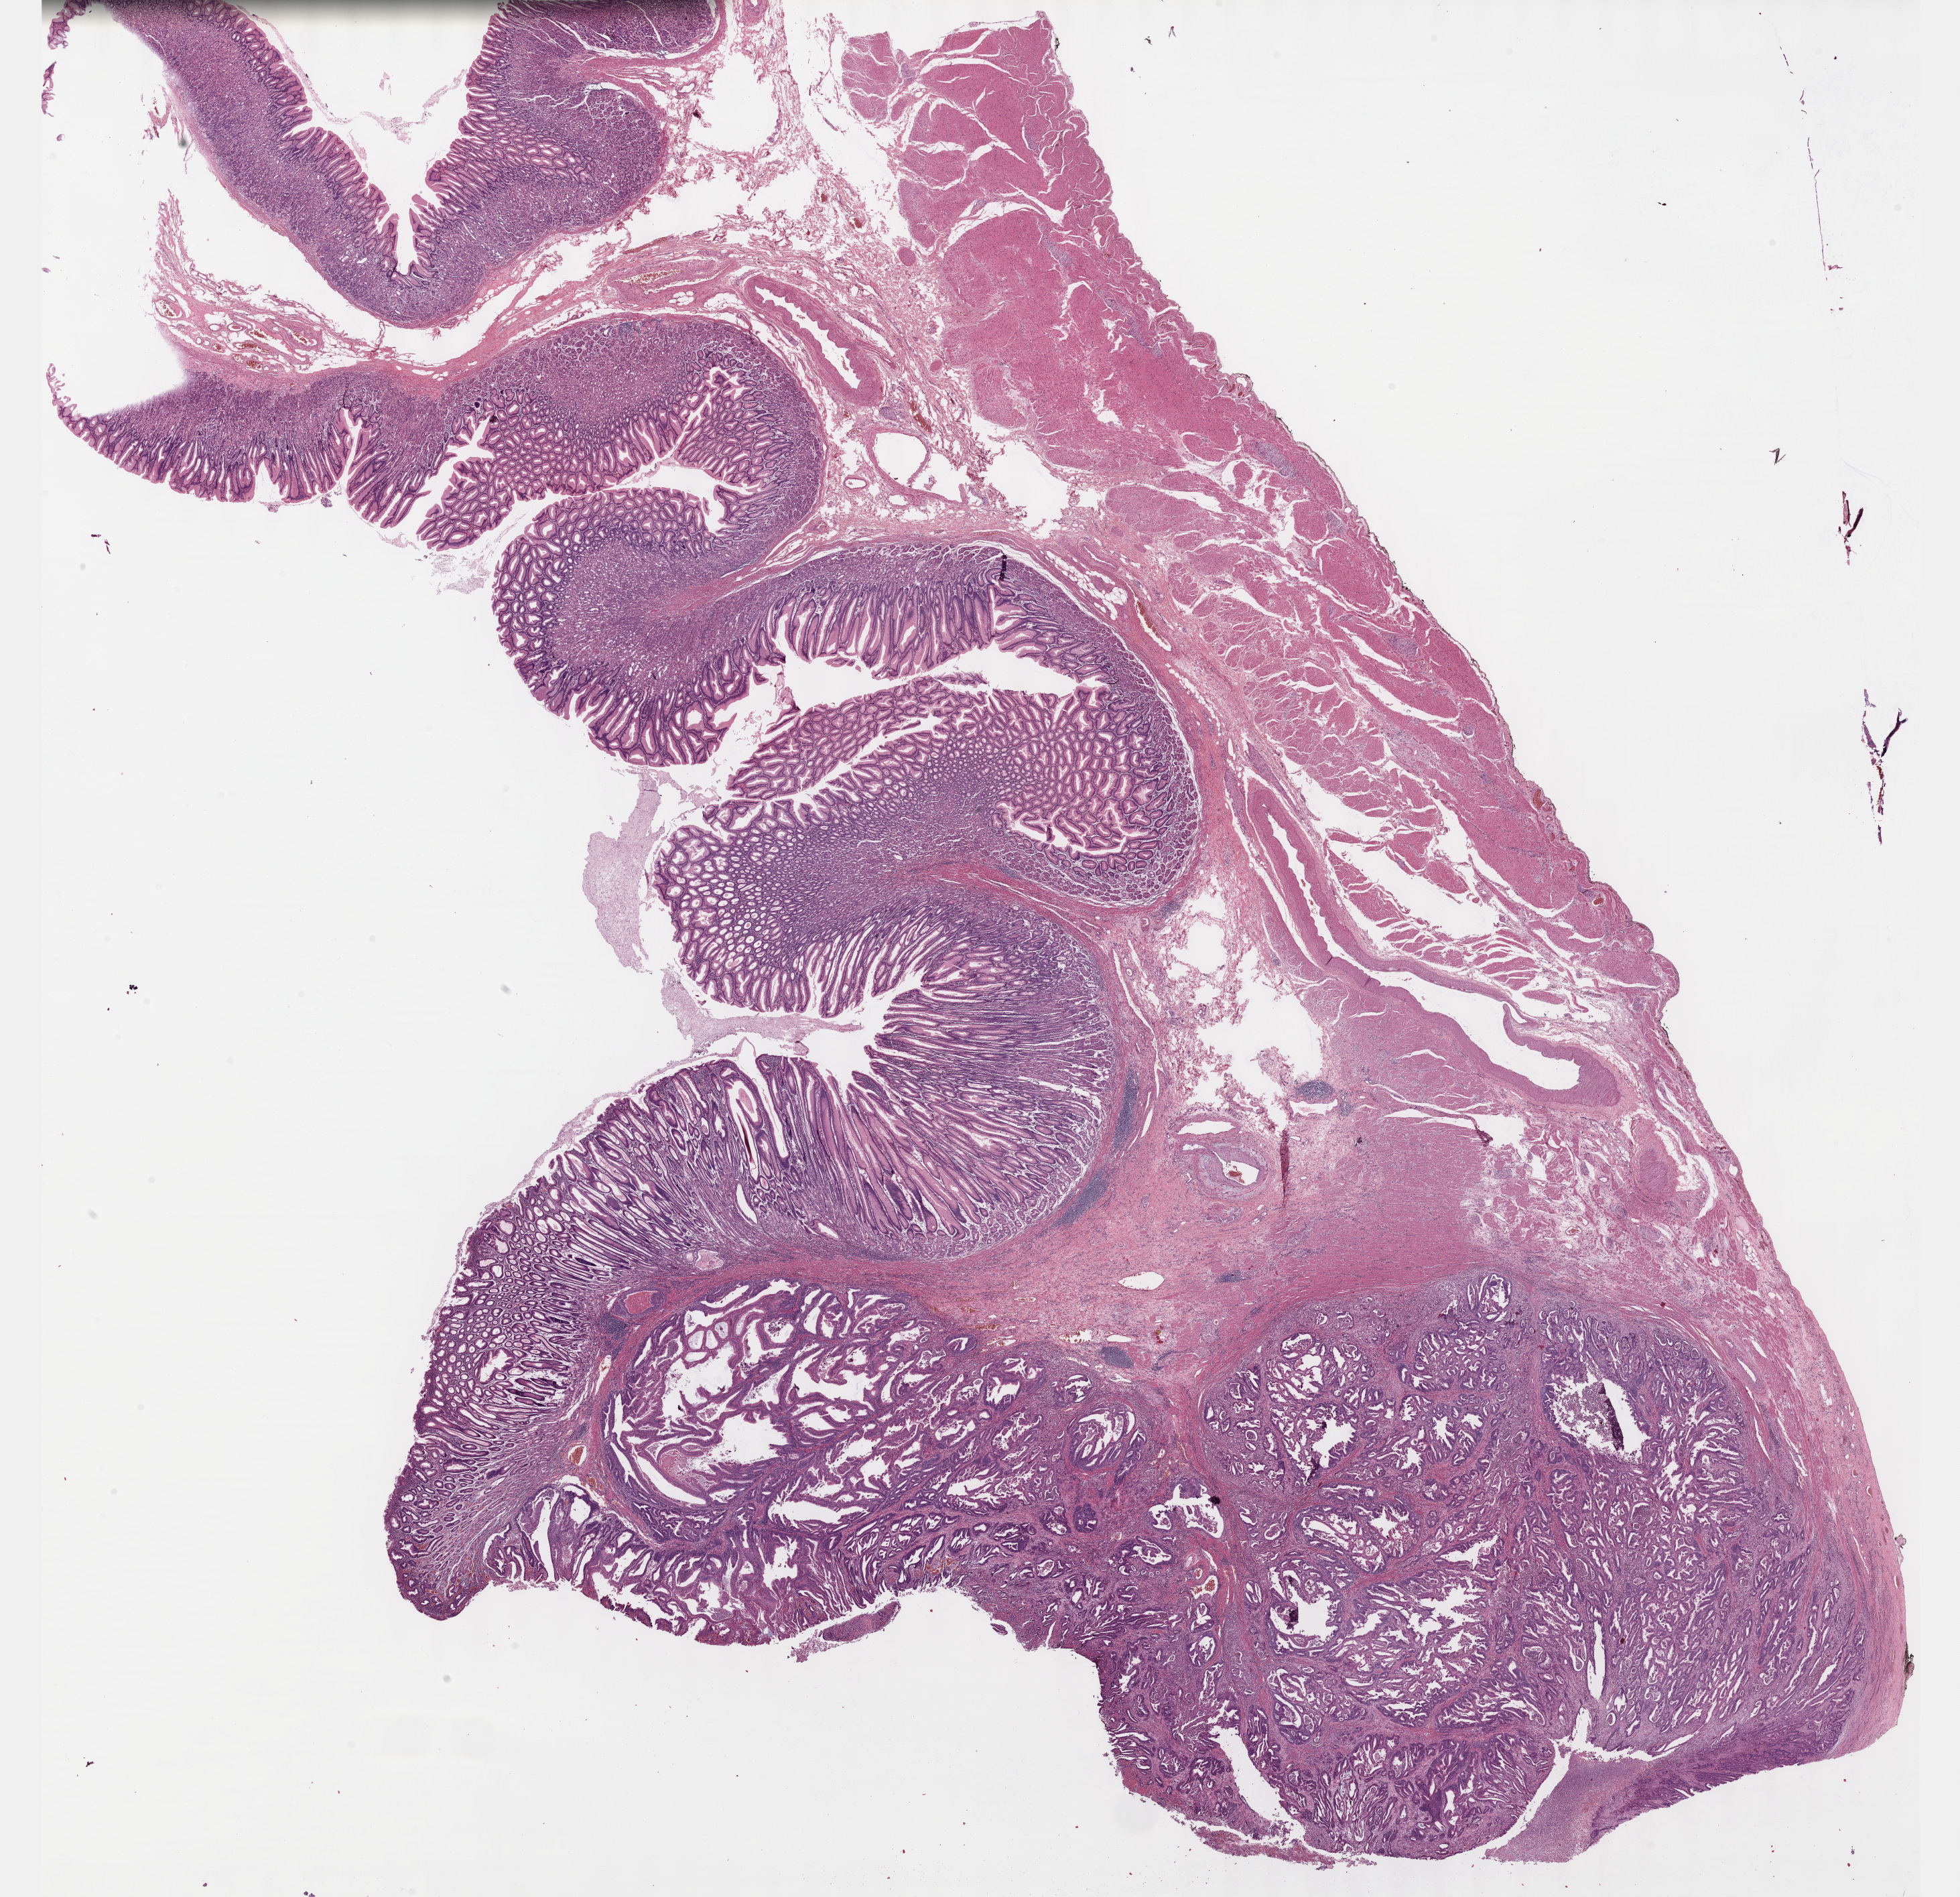
H&E whole-slide image — whole scanned area (about 23.6 x 22.9 mm, acquisition: 40x scan) shown as a low-resolution overview, formalin-fixed paraffin-embedded (FFPE) diagnostic section, sample: primary tumour, stomach. Male, age 67 years at initial diagnosis.
Histologic diagnosis: Tubular adenocarcinoma.